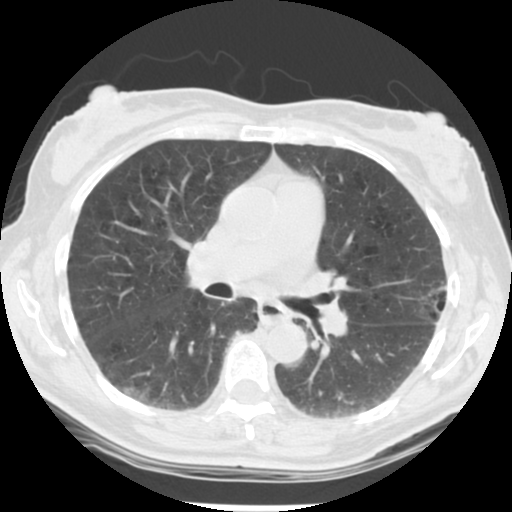
Low-dose screening chest CT, axial slice, second screening round (one year after baseline), lung window (W 1500 / L -600 HU), standard (soft-tissue) reconstruction kernel (STANDARD), slice 125 of 223 in the series, 512 × 512 image matrix. Female, age 61 years at enrolment. Current smoker at enrolment.
• Expert reader's lesion annotation, bounding box [x1, y1, x2, y2] px = [401, 270, 465, 331].
• Screening reader's record for this exam (one nodule recorded; not confirmed to be the boxed lesion): non-calcified nodule or mass ≥4 mm, left upper lobe, 15 × 15 mm, poorly defined margins, mixed attenuation, pre-existing on the prior screen: no.
• Official screen result: positive, other.
• Participant outcome: lung cancer diagnosed 152 days after this screen — bronchiolo-alveolar adenocarcinoma, NOS, left upper lobe, well differentiated (G1), stage IA (AJCC 6th edition), 11 mm at pathology.